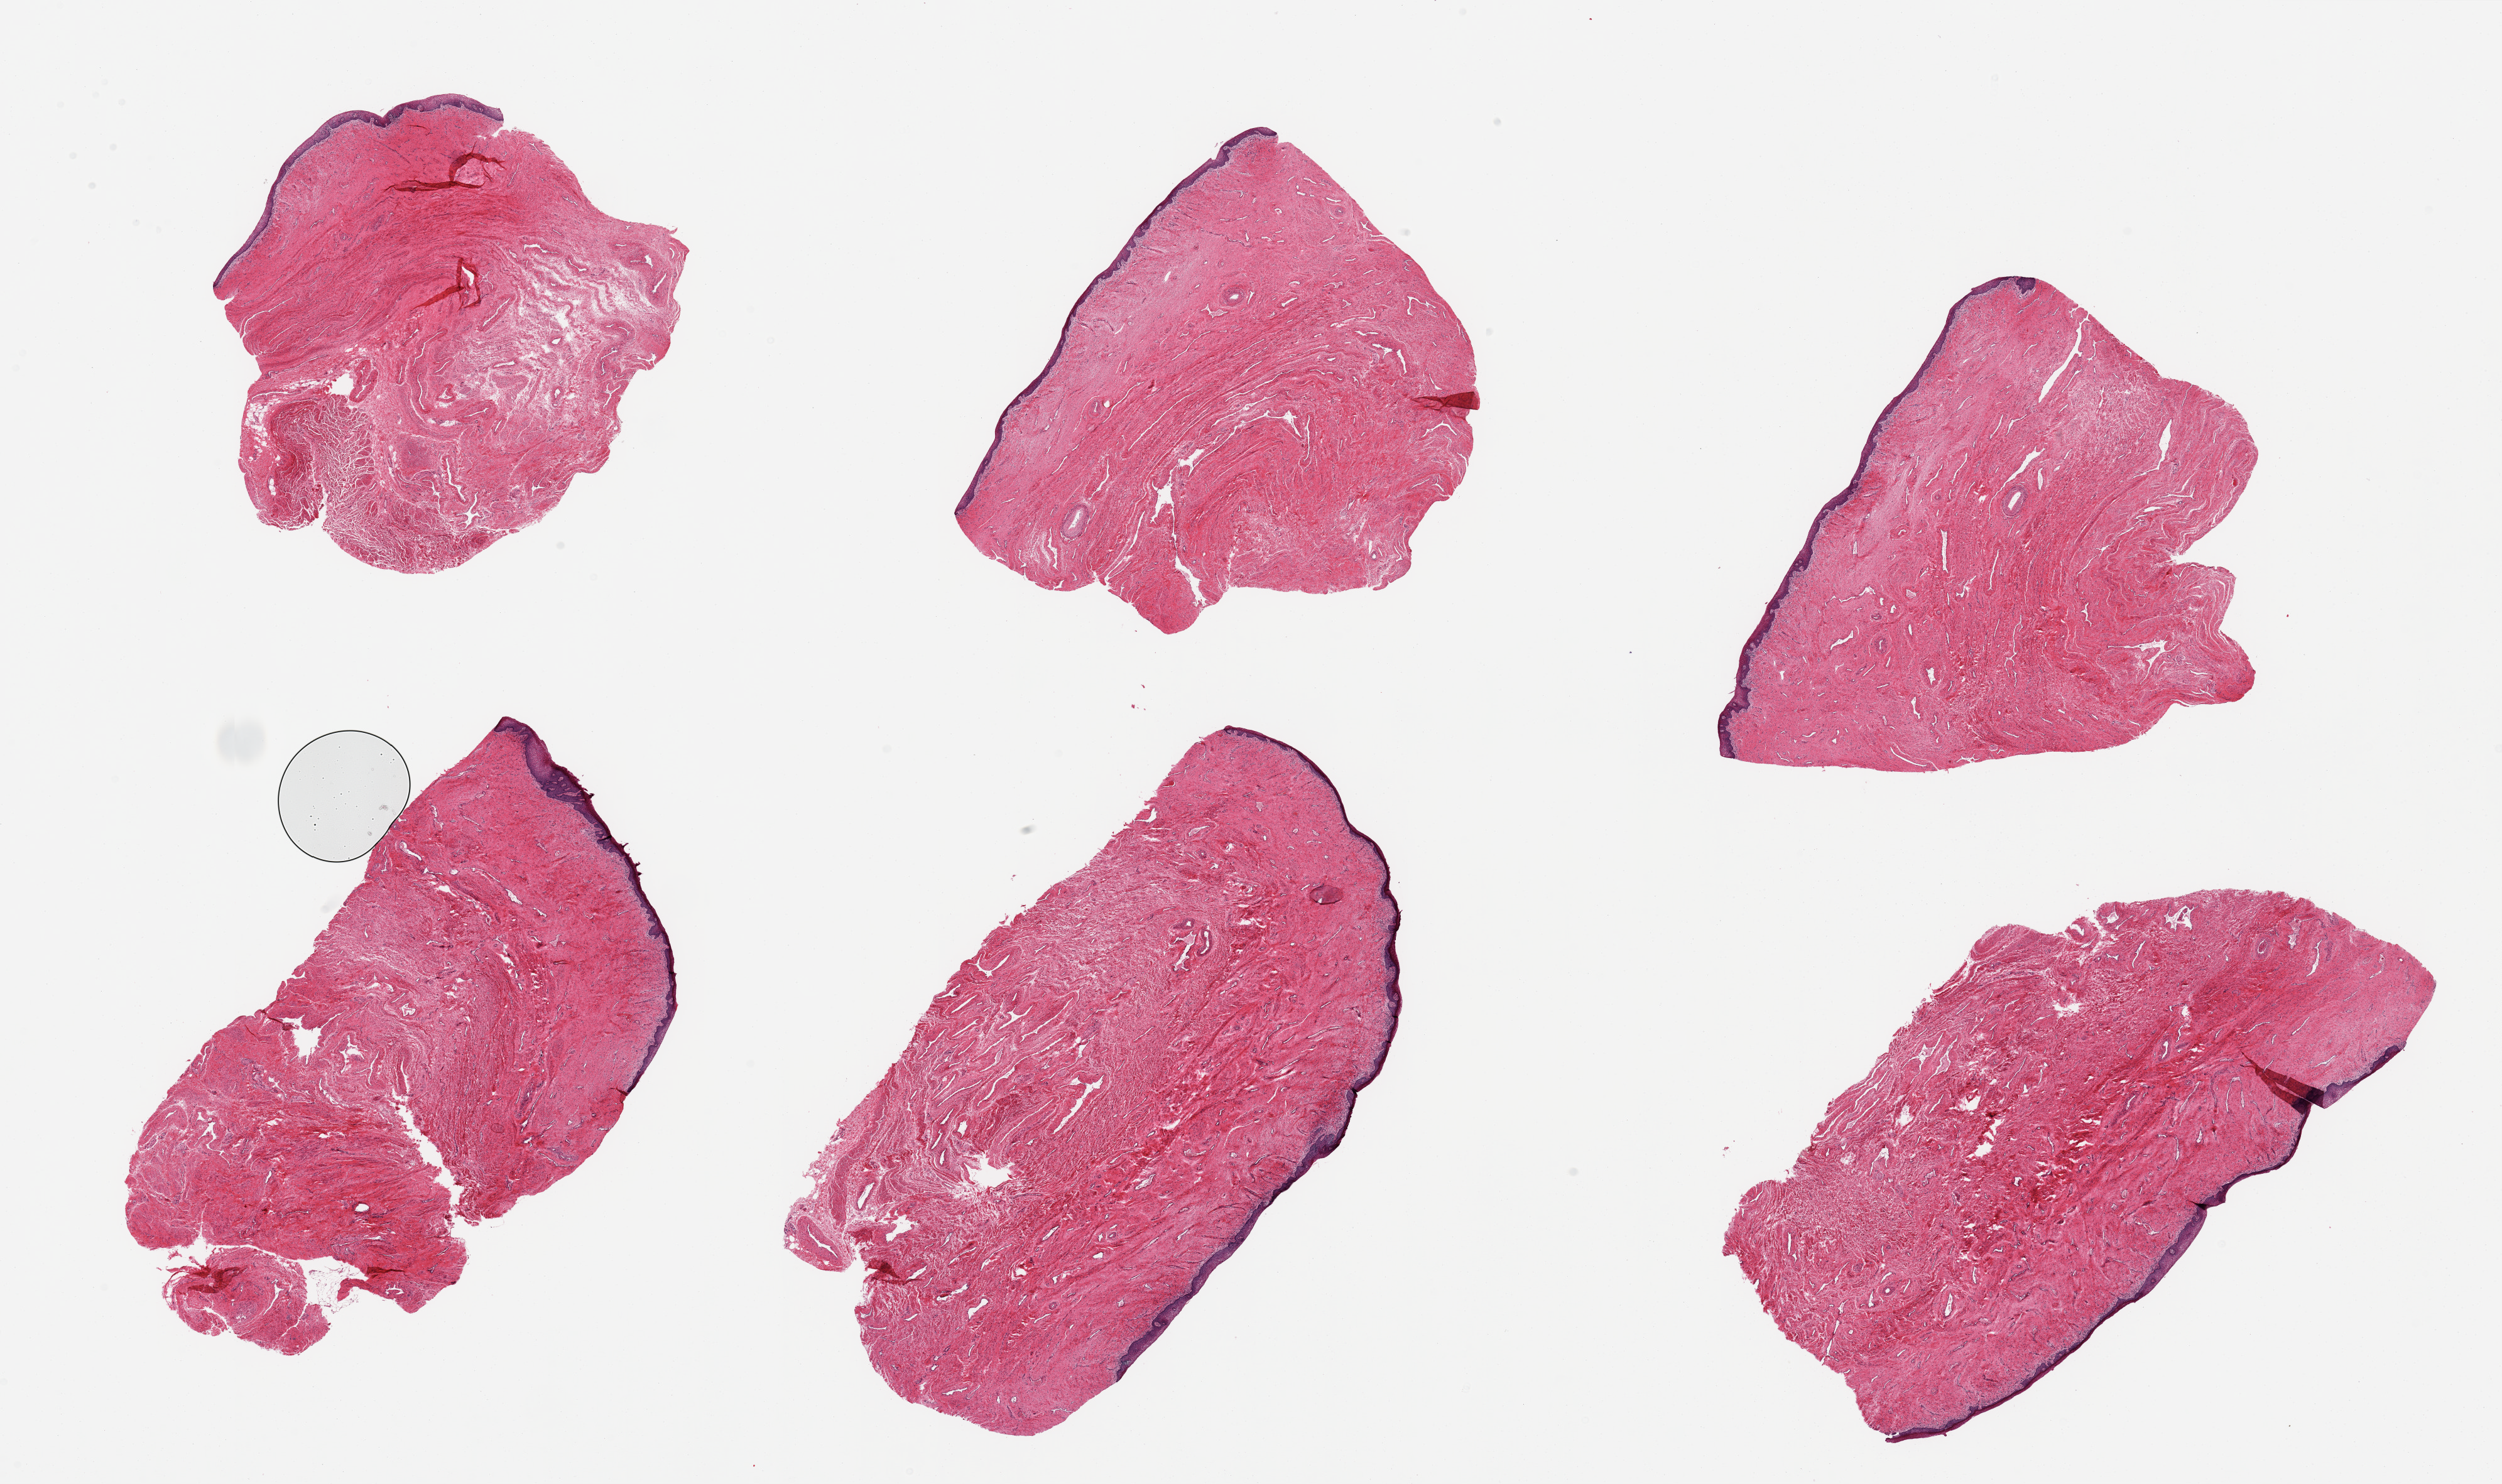
Whole-slide image, H&E stain, brightfield, whole scanned area (about 31.5 x 18.7 mm) shown as a low-resolution overview; PAXgene-fixed, paraffin-embedded tissue; target tissue: vagina; donor tissue sample. Donor sex: female.
Review note (as recorded): 6 pieces.